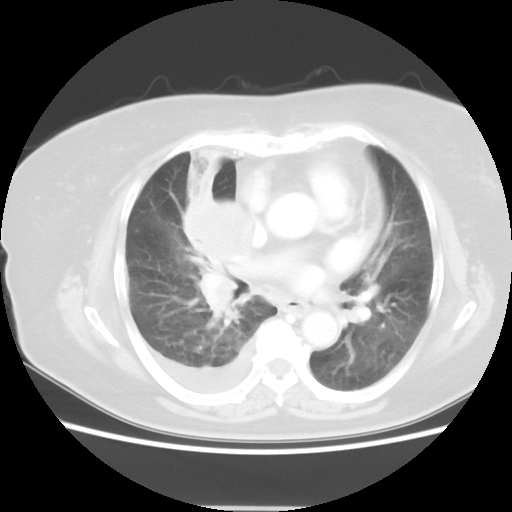
Chest CT, one axial slice. Slice 26 of 48 in the series (ordered by position). Reconstruction kernel STANDARD. Lung window (W 1500 / L -600 HU). 5 mm slice thickness. 512 × 512 image matrix. Female patient, age 73 years. From the clinical record (not read from this slice): clinical TNM (as recorded): T3 N3 M1b.
Annotated regions visible in this slice (rectangle marked by the reading radiologist):
- lung tumour (recorded histology: small cell carcinoma): bounding box [x1, y1, x2, y2] px = [181, 152, 254, 310]